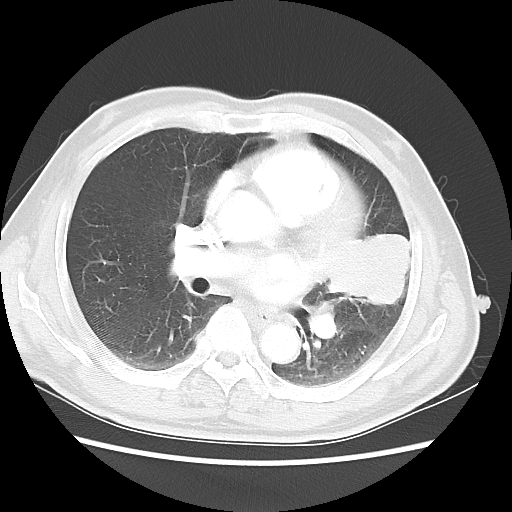
Chest CT, one axial slice; slice 26 of 50 in the series (ordered by position); reconstruction kernel LUNG; 120 kVp; lung window (W 1500 / L -600 HU); 512 × 512 image matrix, field of view 360 × 360 mm. Male patient, age 69 years. Case-level facts recorded for this patient, not image findings: clinical TNM (as recorded): T3 N1 M1a.
Annotated regions visible in this slice (rectangle marked by the reading radiologist):
- lung tumour (recorded histology: squamous cell carcinoma): box from (x=327, y=219) to (x=436, y=321) px